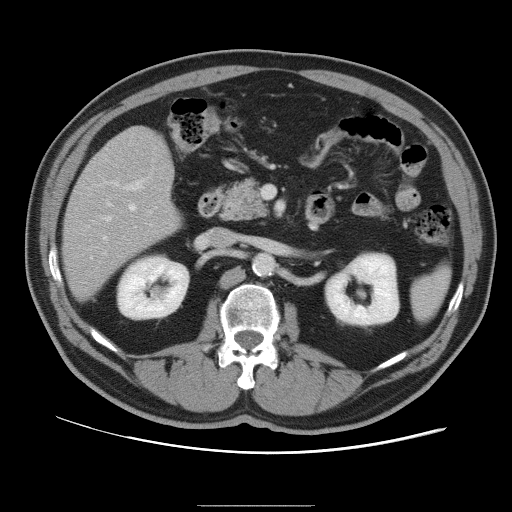
Contrast-enhanced abdominal CT, one axial slice. Slice 46 of 105 in the series (ordered by position). Intravenous contrast given. Soft-tissue window (W 400 / L 40 HU). 512 × 512 image matrix, field of view 399 × 399 mm. Male patient, age 64 years. From the clinical record (not read from this slice): diagnosis: colorectal cancer liver metastases, imaged before liver resection.
Structures marked on this image (outlined manually by an expert reader):
- hepatic veins: bounding box (x1, y1, x2, y2) in pixels: (90, 203, 136, 259)
- liver: (64, 128, 181, 300)
- planned liver remnant (the part of the liver to remain after resection): (66, 129, 181, 300)
- portal vein (with intrahepatic branches): (103, 179, 145, 240)